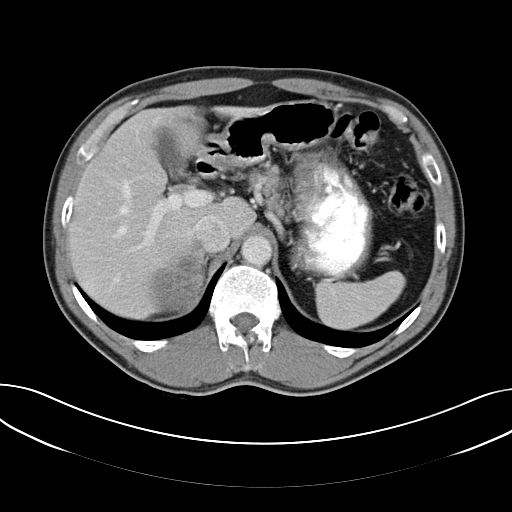
Contrast-enhanced abdominal CT, one axial slice; position 41 of 61 along the scan axis; reconstruction kernel B40f; intravenous contrast given; soft-tissue window (W 400 / L 40 HU); 5 mm slice thickness; 512 × 512 image matrix. Male patient, age 57 years. From the clinical record (not read from this slice): diagnosis: adrenocortical carcinoma; tumour side: right adrenal; tumour size at pathology: 11.2 cm; Ki-67 index: 10 %; stage (as recorded): 3.
Outlined on this slice (semi-automatically segmented with operator editing):
- mass: bounding box (x1, y1, x2, y2) in pixels: (149, 256, 201, 308)